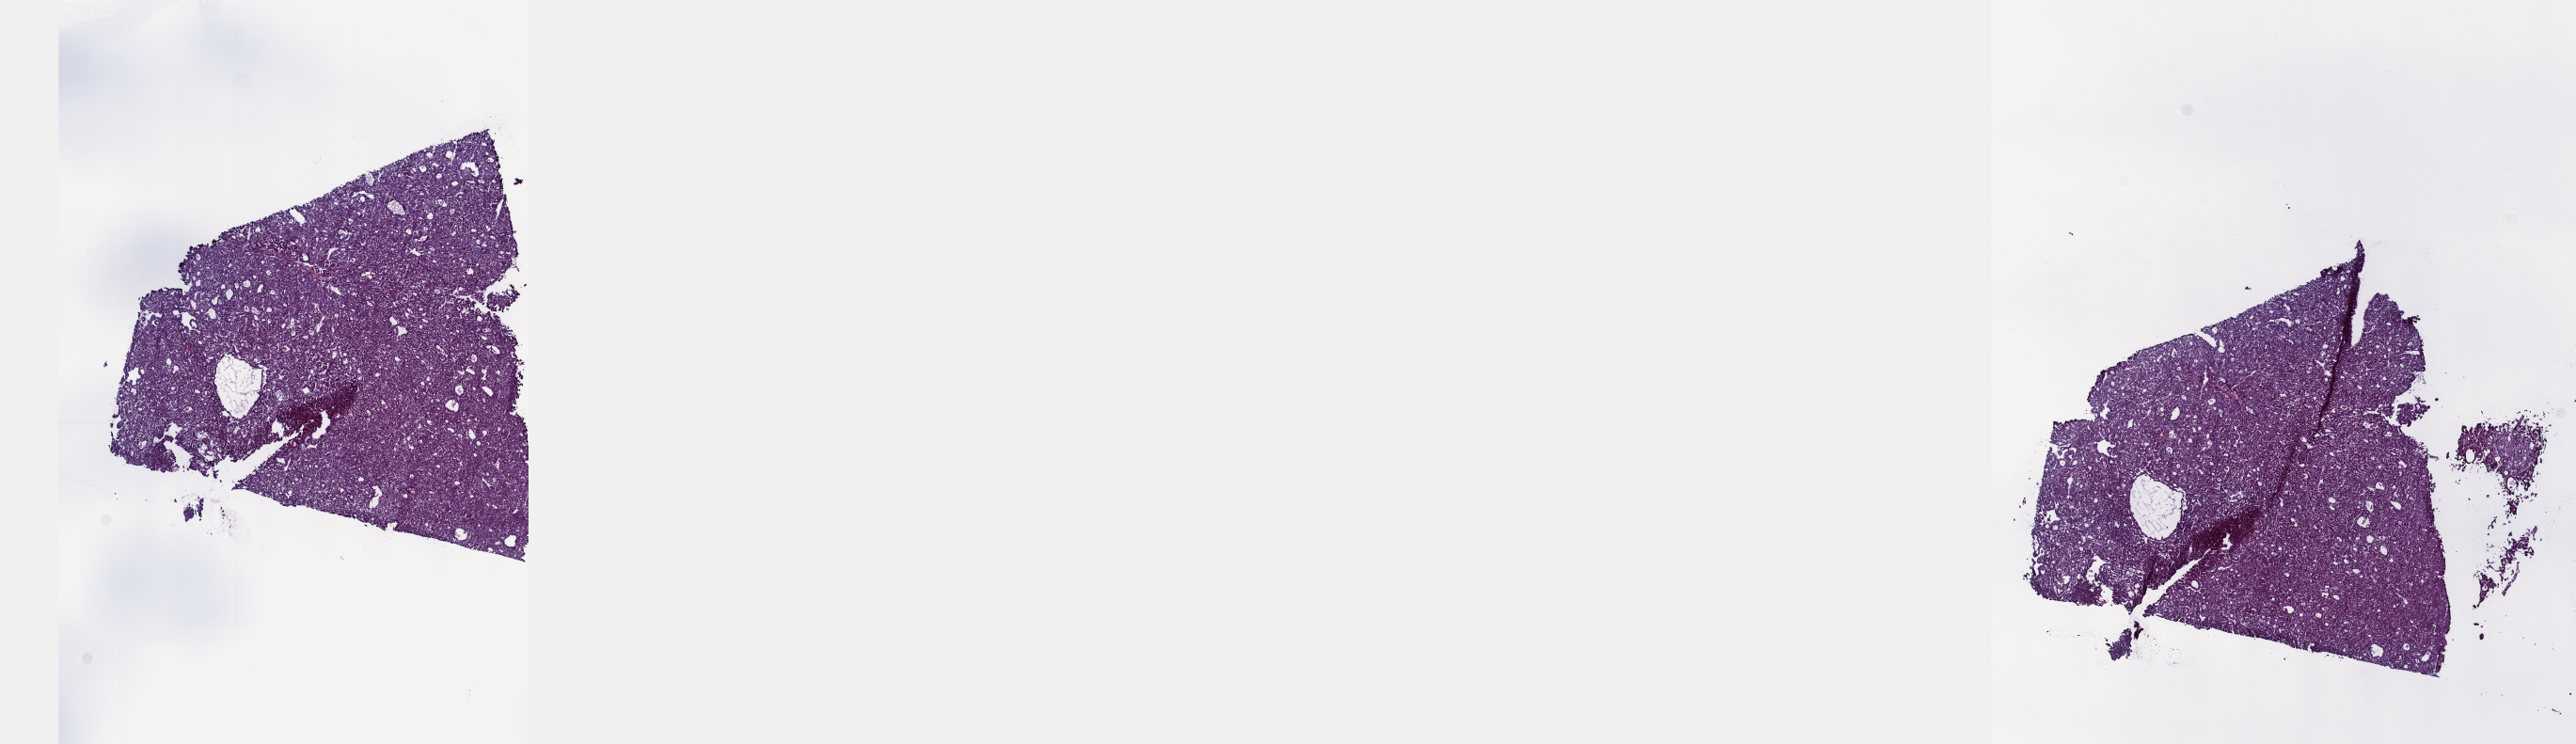
Whole-slide histology image, H&E-stained, a low-resolution overview of the entire scanned area, about 22.1 x 6.4 mm (slide scanned at 40x). Frozen section from the top of the tissue portion. Primary tumour sample from the liver. Patient: male, age at initial diagnosis 50 years. Composition of this section per pathologist review: tumour cells 85%, tumour nuclei 85%.
Histologic diagnosis: Hepatocellular carcinoma, NOS.